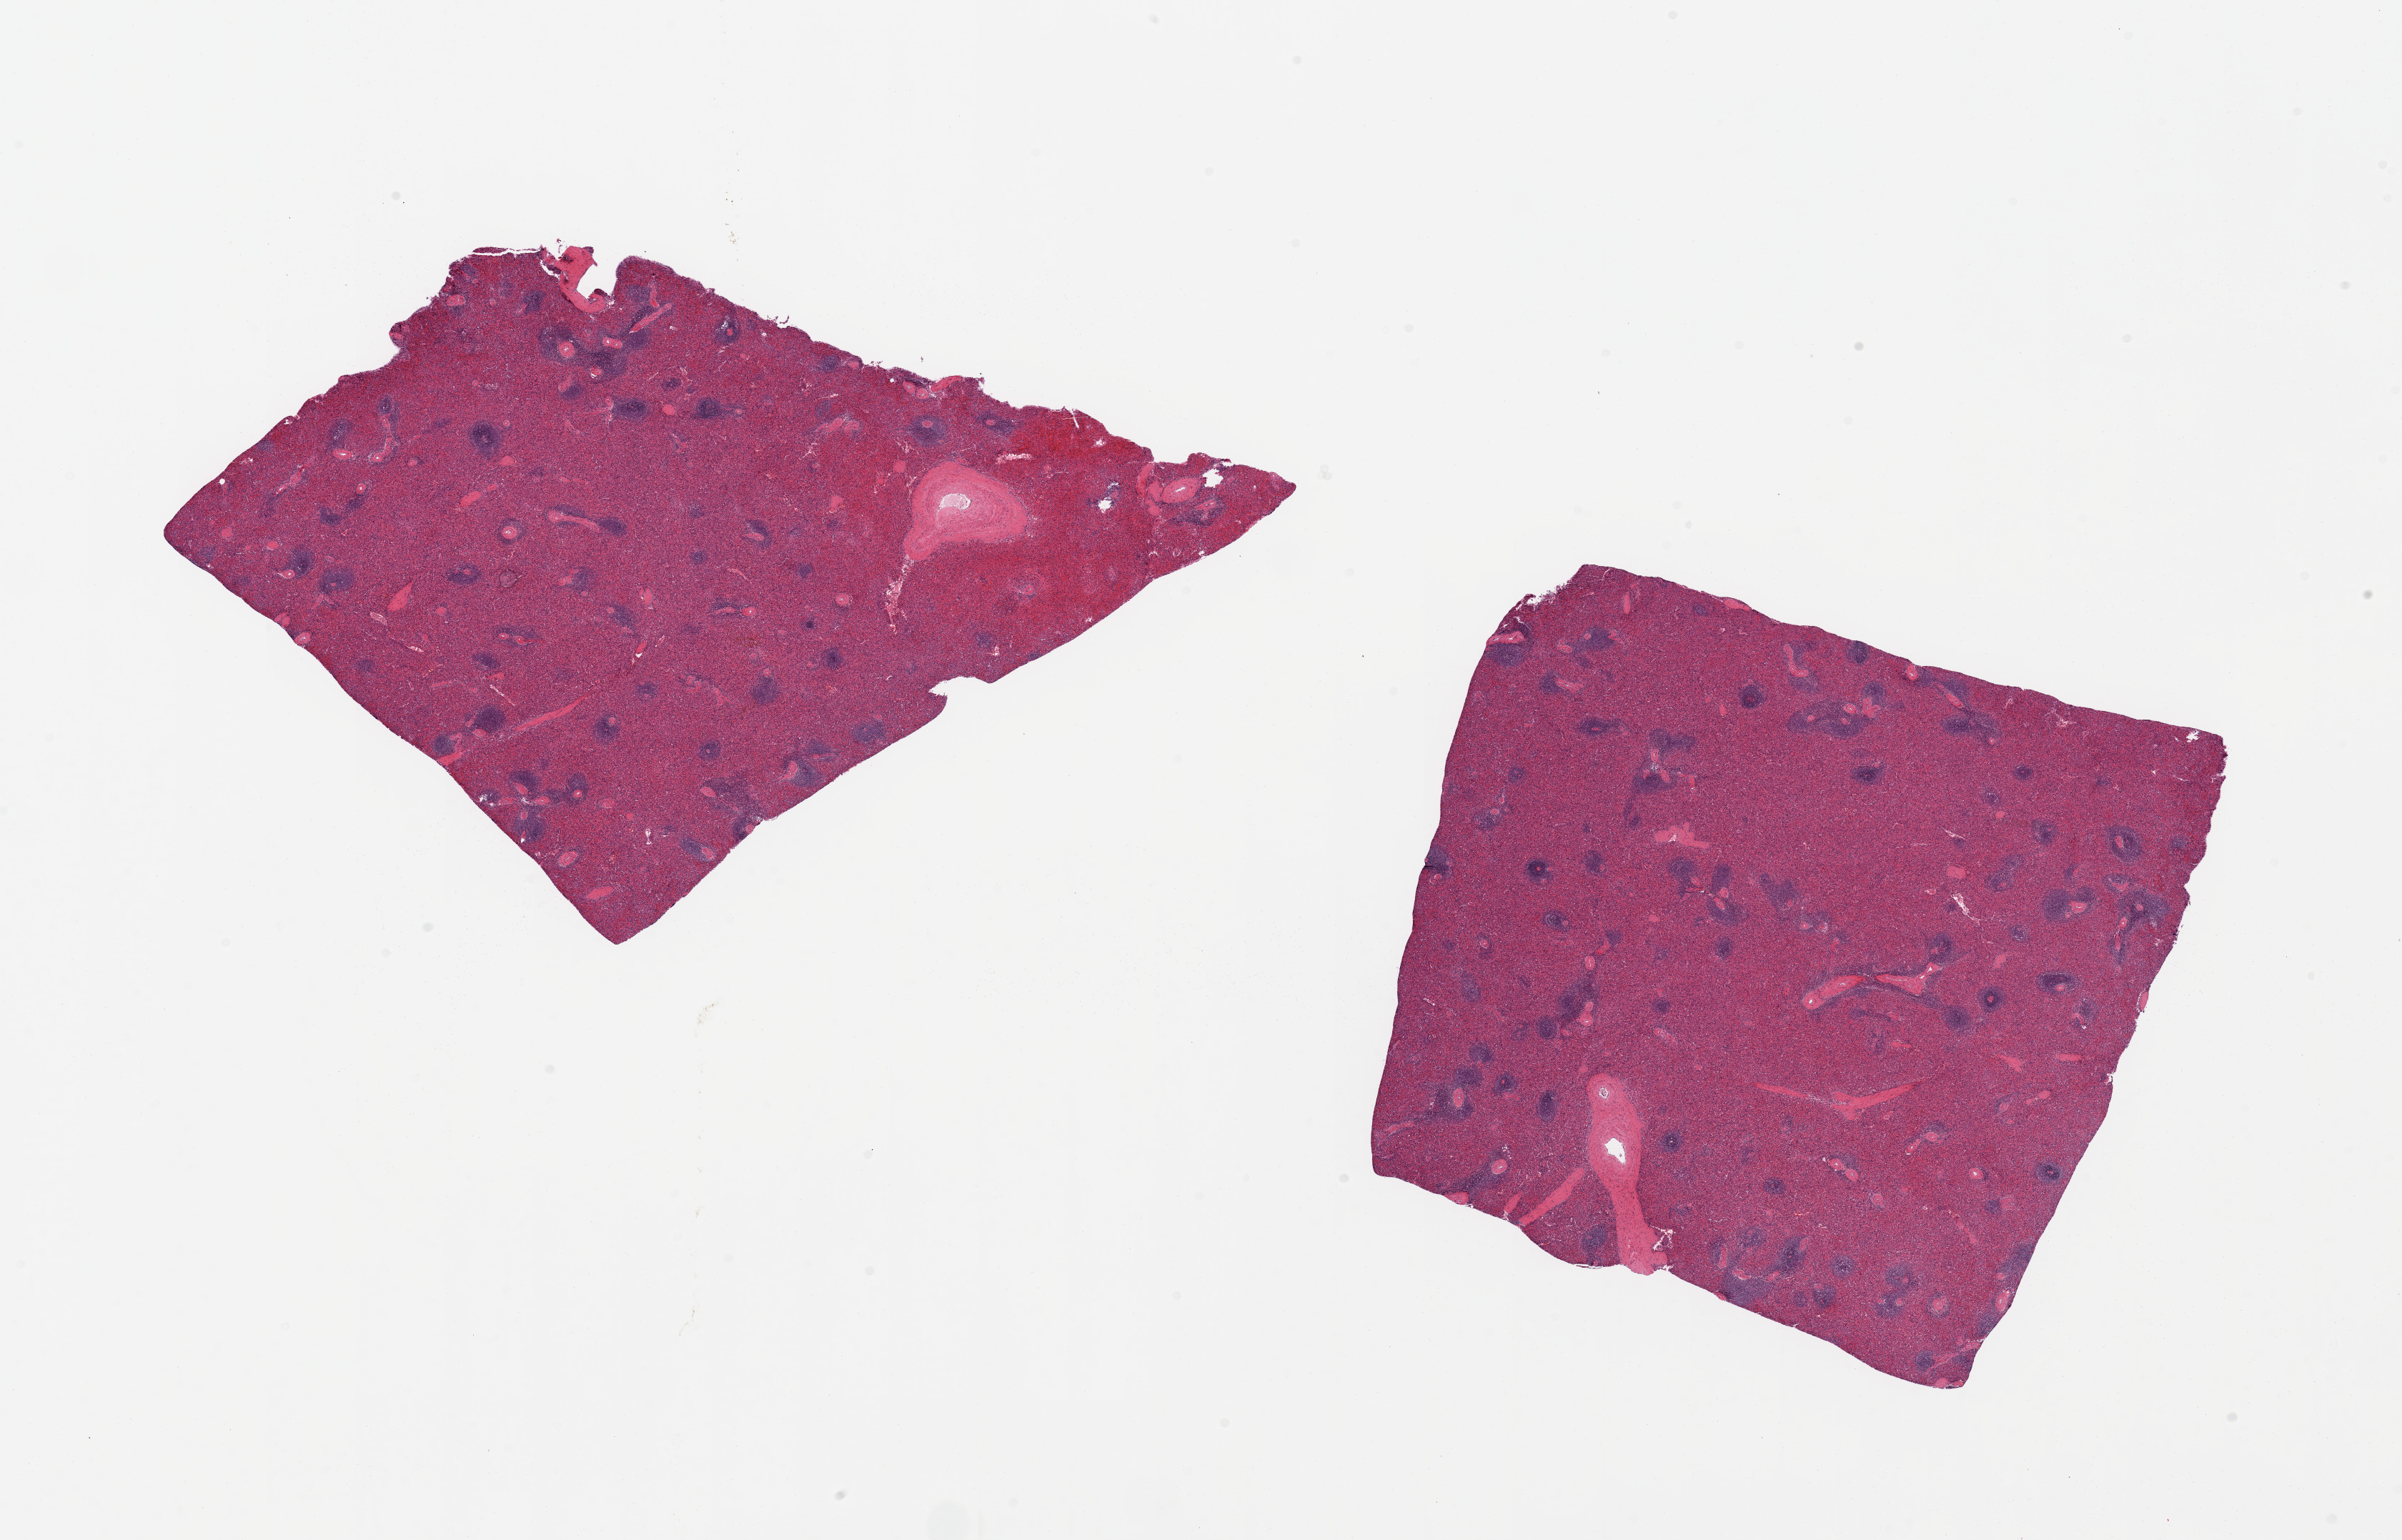
Whole-slide image, H&E stain, shown as a low-resolution overview of the whole scanned area (about 26.6 x 17.0 mm). PAXgene-fixed paraffin-embedded (PFPE) section. Sampled site (target tissue): spleen. Tissue donor sample. Donor: female.
Pathologist's review note for this sample: 2 pieces.